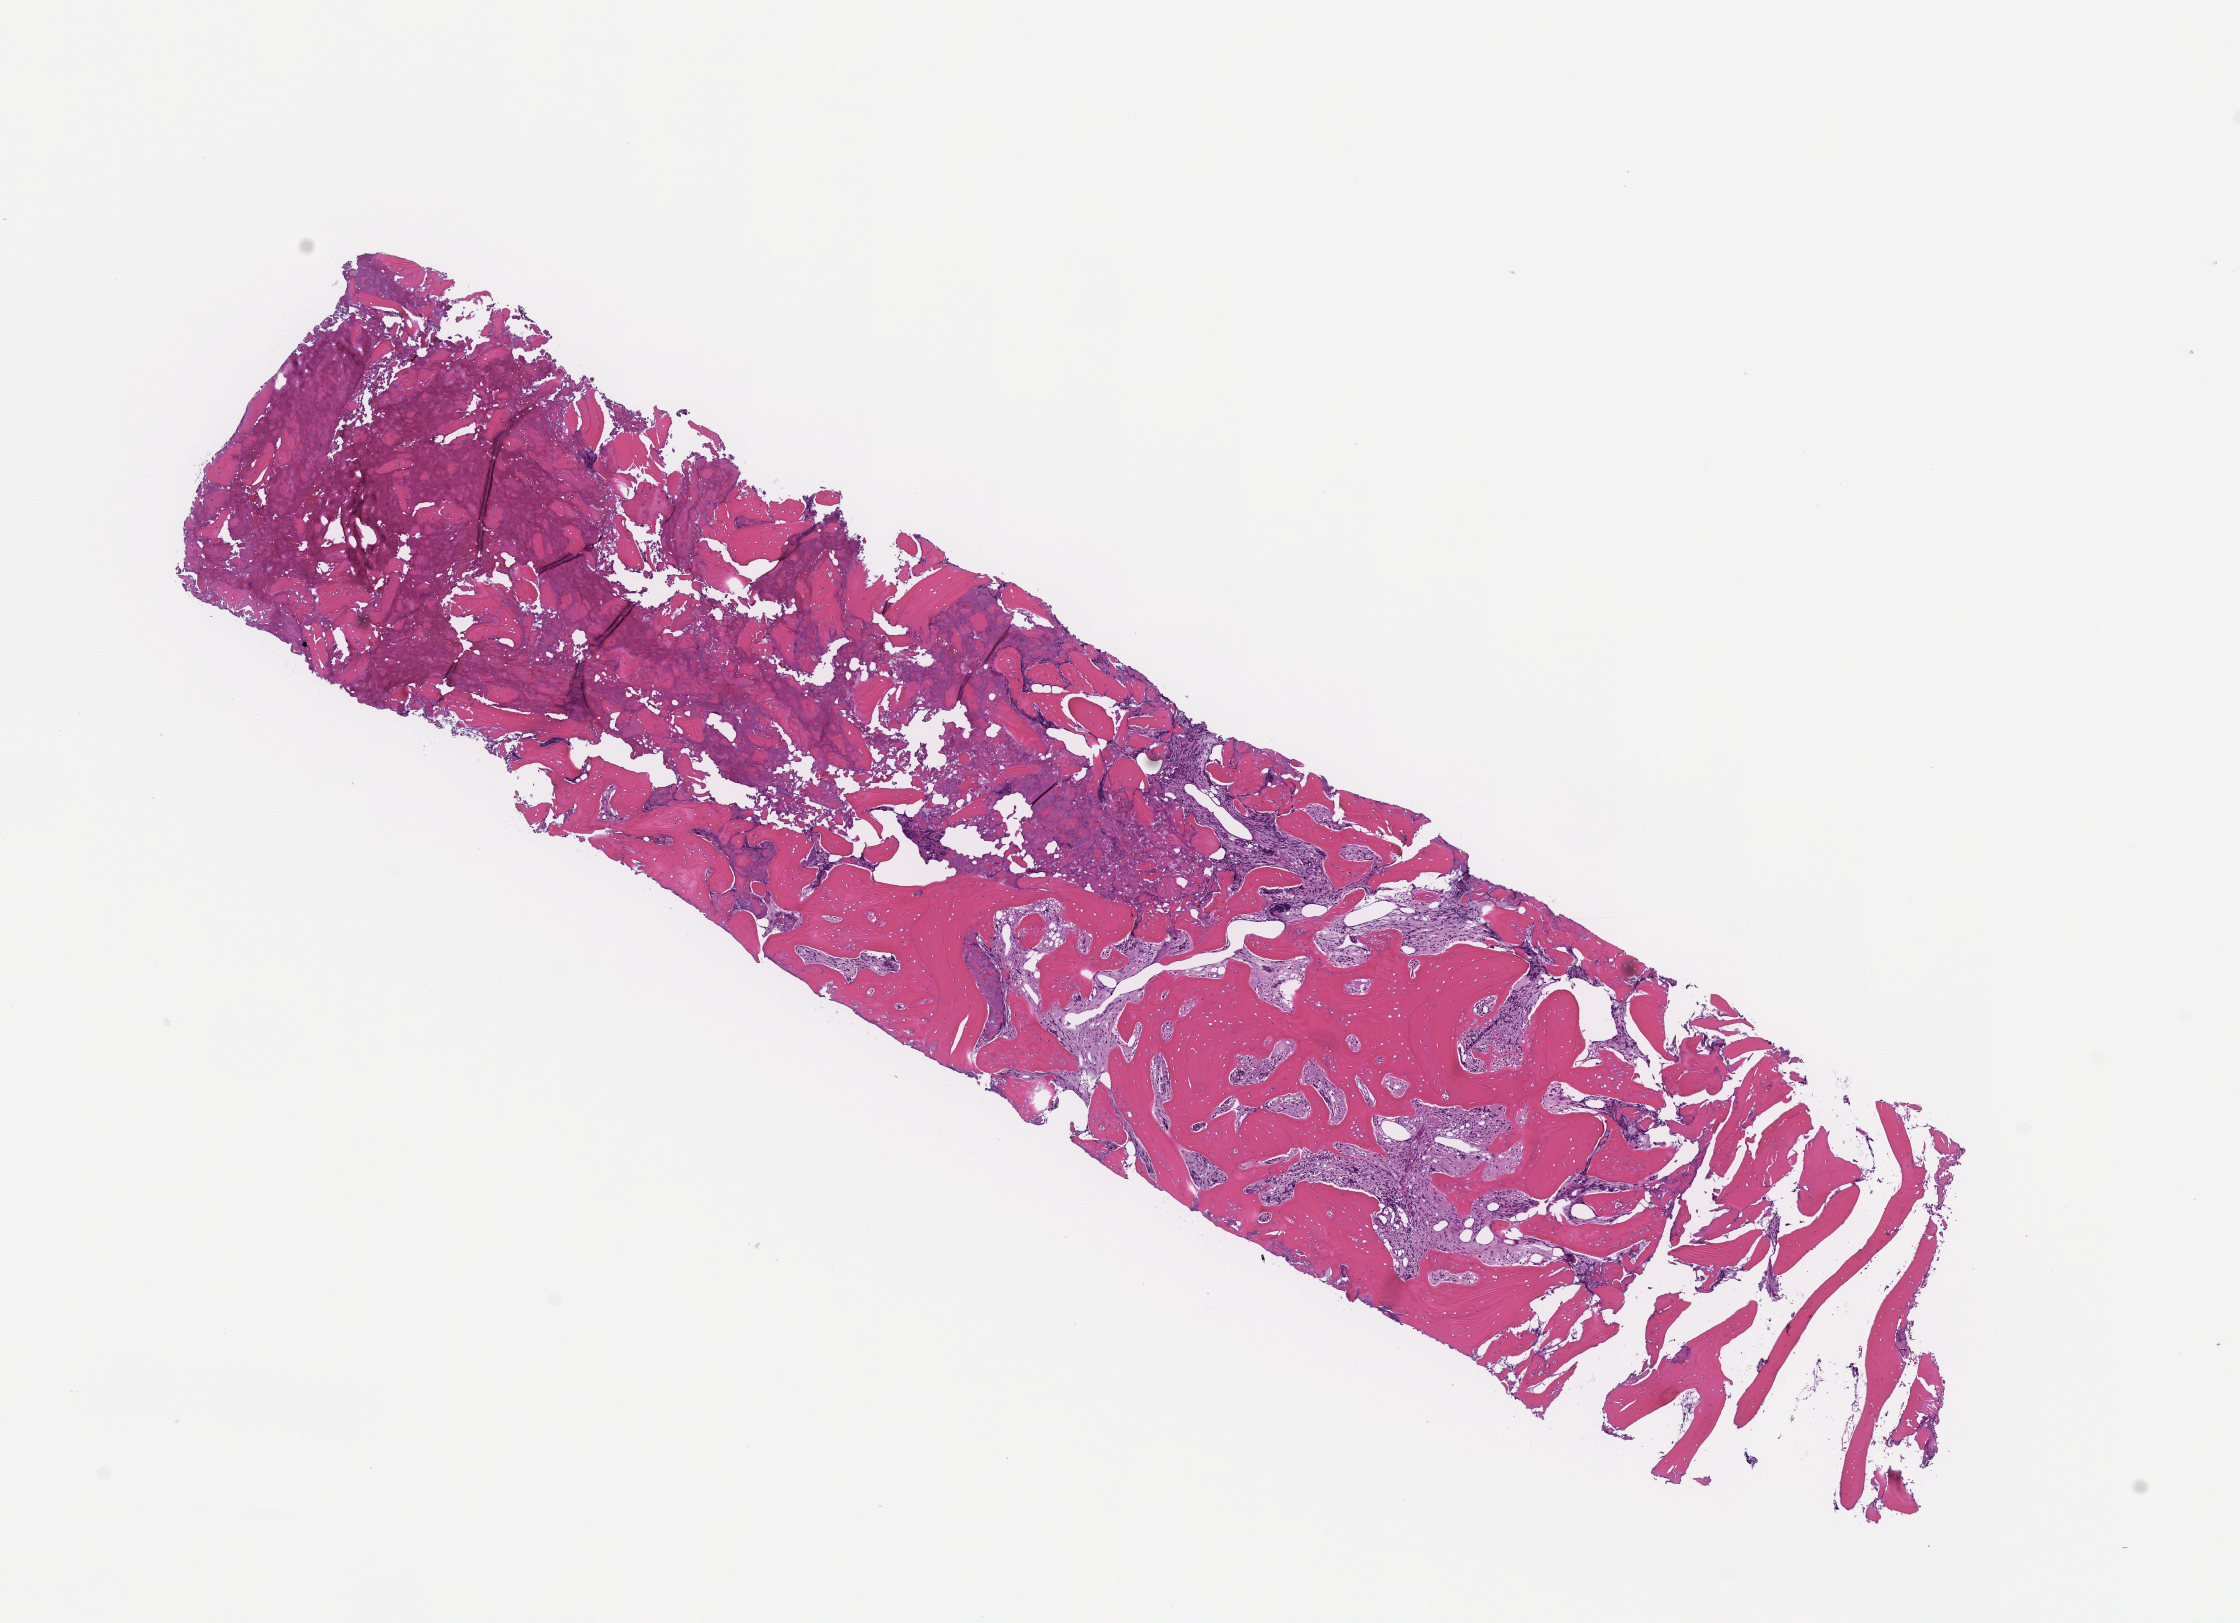
Digitized haematoxylin and eosin-stained section — shown as a low-resolution overview of the whole scanned area (about 9.0 x 6.6 mm); formalin-fixed, paraffin-embedded (FFPE) tissue; site: breast; archival tissue. Female patient.
• patient diagnosis: Invasive Breast Carcinoma